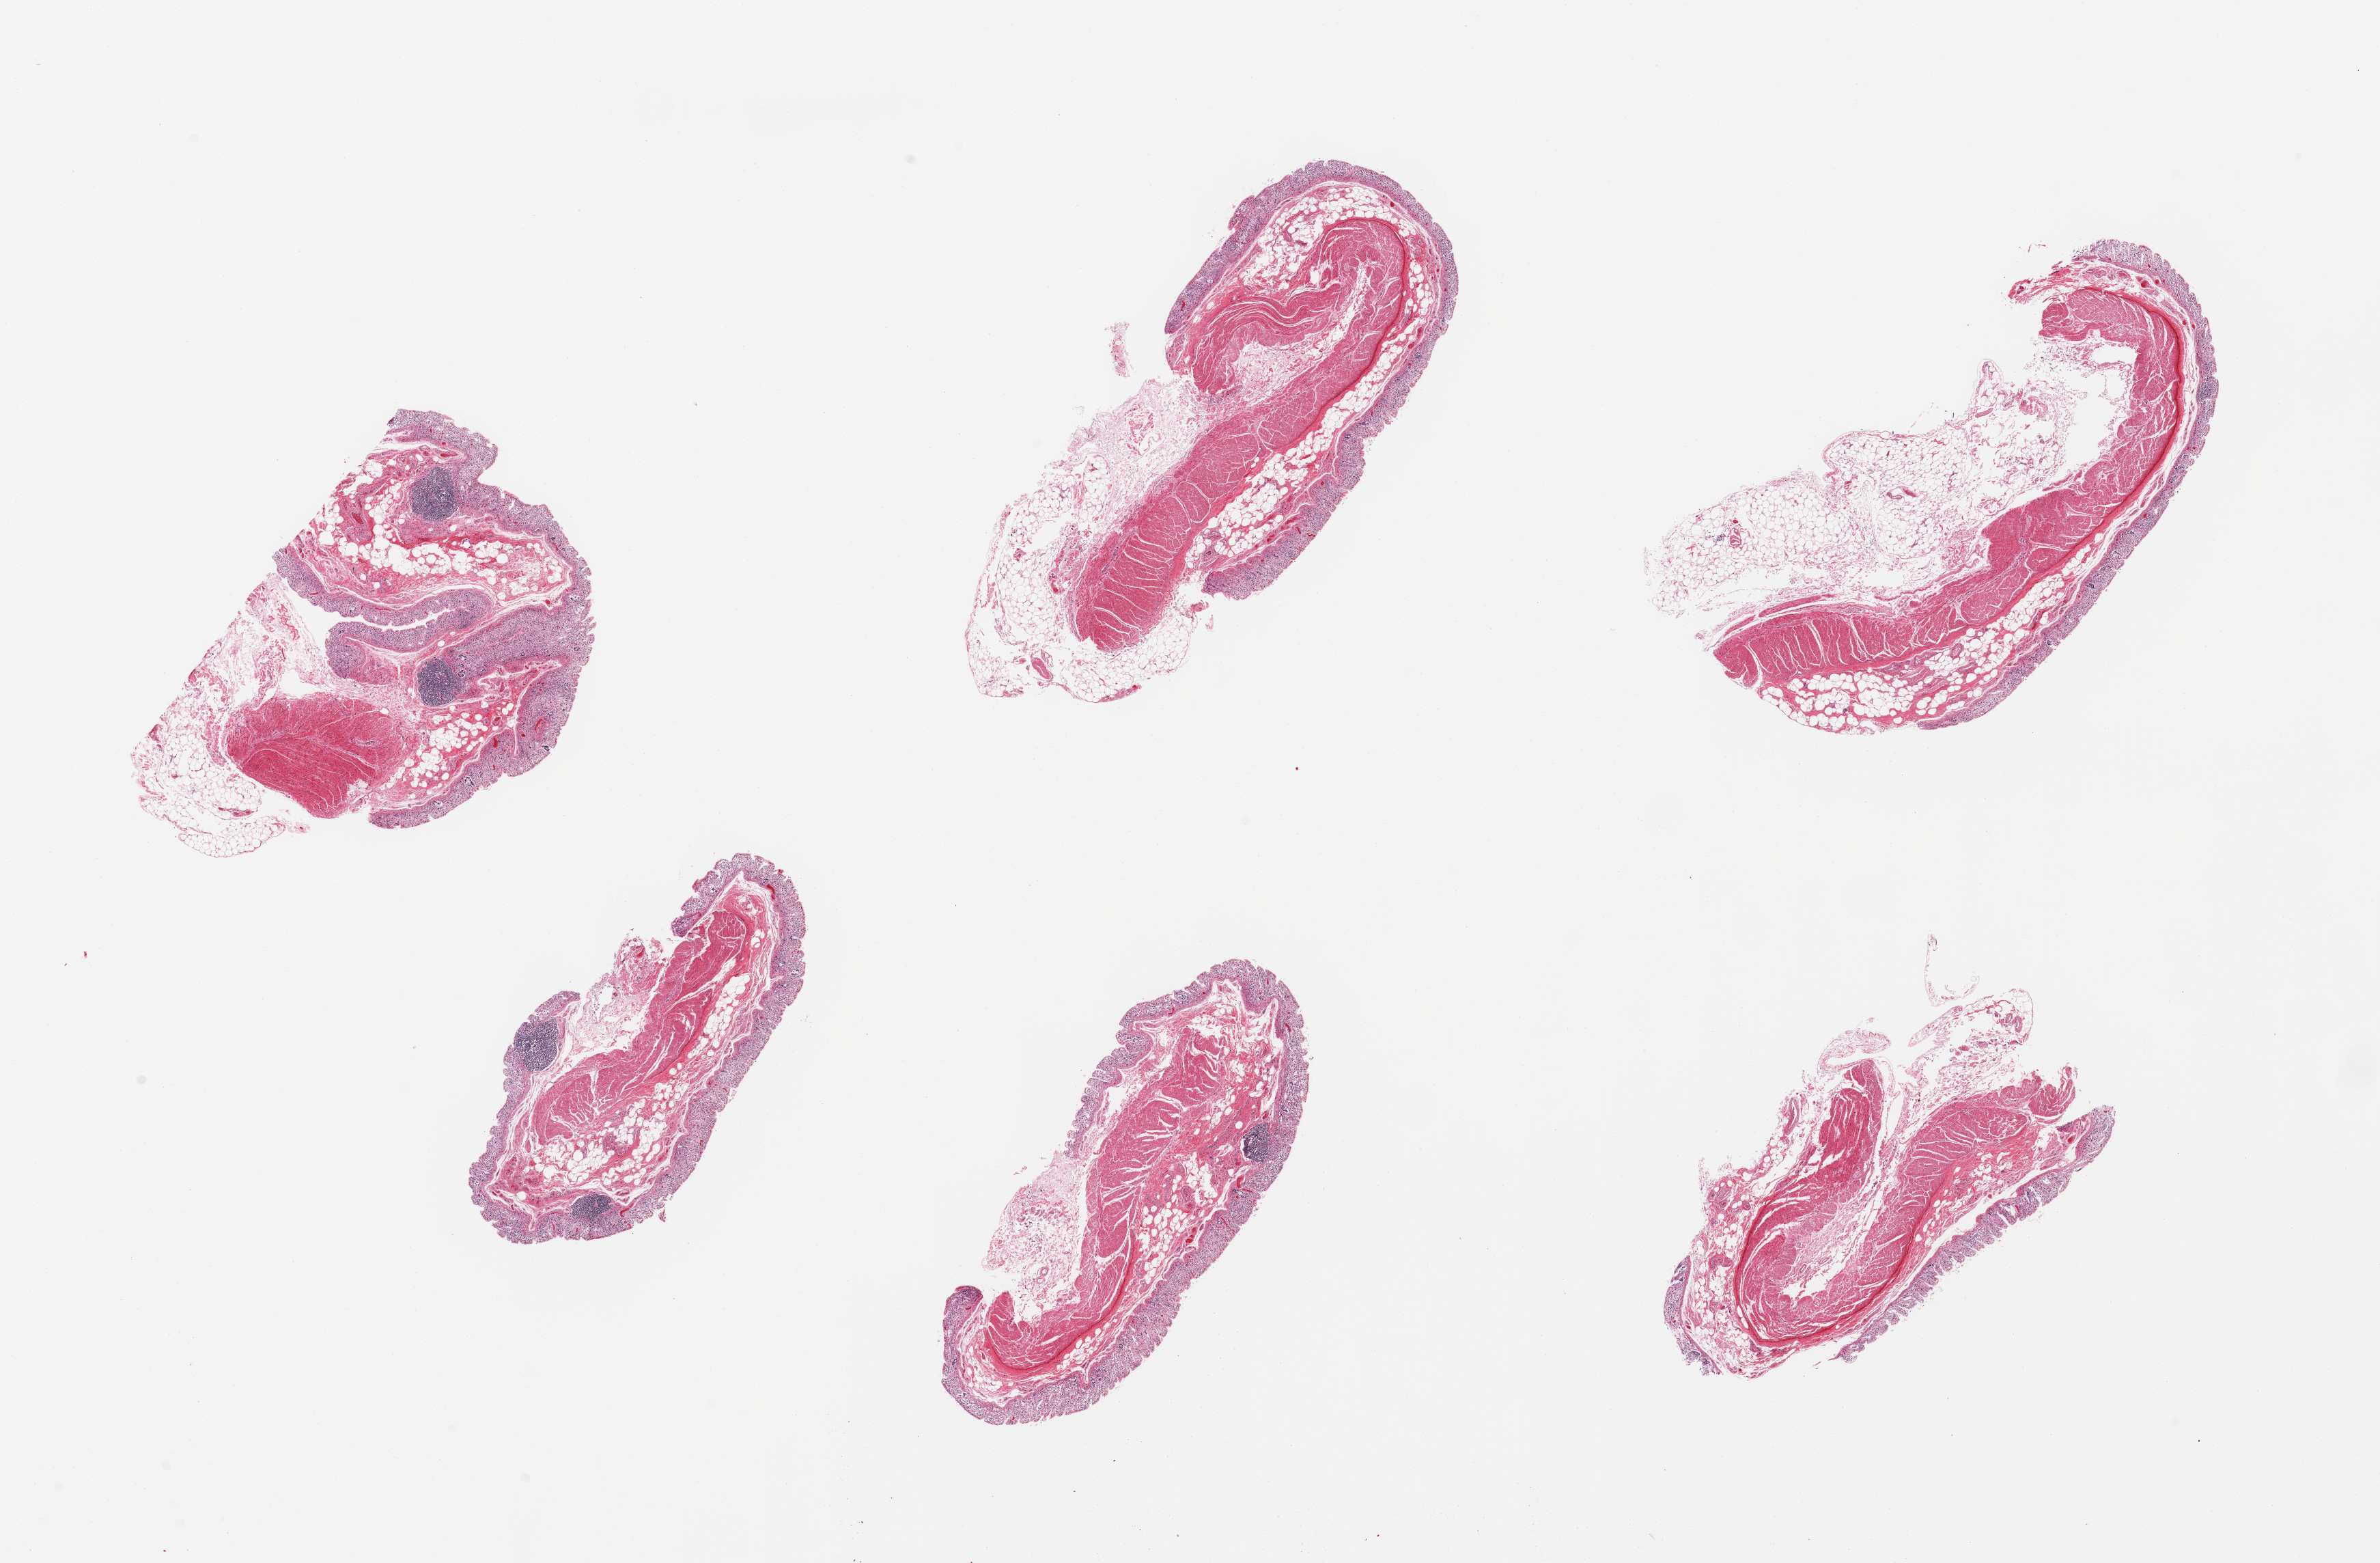
H&E whole-slide image — shown as a low-resolution overview of the whole scanned area (about 27.6 x 18.1 mm, from a 20x scan). PAXgene-fixed, paraffin-embedded tissue. Section of transverse colon (target tissue). Donor tissue sample. Male donor.
Review note (as recorded): 6 pieces; muscularis and autolyzed mucosa; serosa with external fat up to 1.9mm.